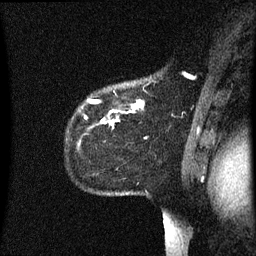
Breast MRI (dynamic contrast-enhanced), one sagittal slice; position 49 of 60 along the scan axis; dynamic contrast-enhanced series, image 2 of 3 at this slice position (ordered by acquisition); 1.5 T; TE 4.2 ms, TR 8.4 ms; 2.2 mm slice thickness; 256 × 256 image matrix, field of view 200 × 200 mm. Patient: female, 35 years. From the clinical record (not read from this slice): setting: breast cancer imaged before/during neoadjuvant chemotherapy; receptor status: HER2-positive.
Structures marked on this image (semi-automatically segmented with operator editing):
- analysis volume of interest (the breast-tissue region the enhancement analysis was run in; not a lesion): box from (x=68, y=84) to (x=145, y=151) px
- tumour enhancement mask (voxels above the 70 % enhancement threshold inside the analysis volume of interest): (x=89, y=100)–(x=144, y=125)